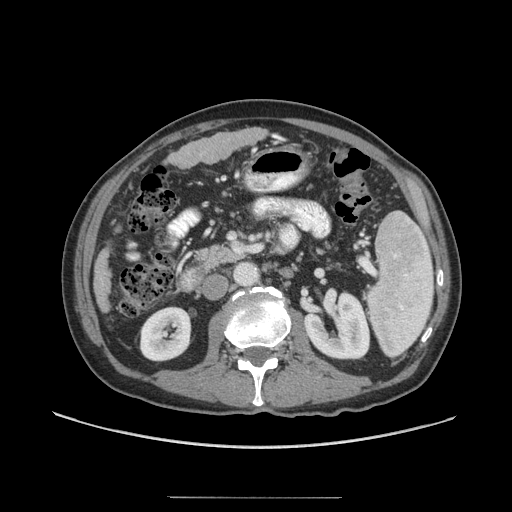
Contrast-enhanced abdominal CT (liver protocol), one axial slice. Slice 14 of 71 in the series (ordered by position). Reconstruction kernel STANDARD. Soft-tissue window (W 400 / L 40 HU). 512 × 512 image matrix, field of view 400 × 400 mm. Case-level facts recorded for this patient, not image findings: diagnosis: hepatocellular carcinoma (patient treated with transarterial chemoembolisation; whether this scan precedes or follows treatment is not stated here); TNM stage (as recorded): Stage-I; Child-Pugh class: A; tumour nodularity: uninodular; tumour size: 3.5 cm.
Structures marked on this image (semi-automatic segmentation, software-assisted and operator-edited):
- liver parenchyma outside the tumour (the mass and vessels are separate outlines, so this box may not span the whole liver): box from (x=94, y=128) to (x=266, y=312) px